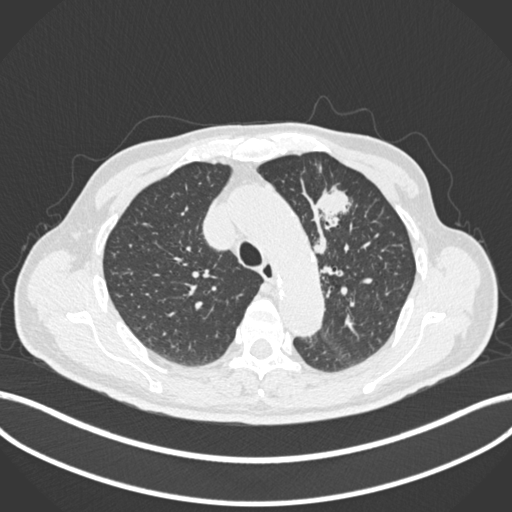
Chest CT, one axial slice; position 183 of 261 along the scan axis; reconstruction kernel B30f; 120 kVp; lung window (W 1500 / L -600 HU); 512 × 512 image matrix. Patient: male, 74 years. Case-level facts recorded for this patient, not image findings: clinical TNM (as recorded): T2b N0 M1c.
Outlined on this slice (rectangle marked by the reading radiologist):
- lung tumour (recorded histology: adenocarcinoma): bounding box [x1, y1, x2, y2] px = [312, 182, 359, 233]